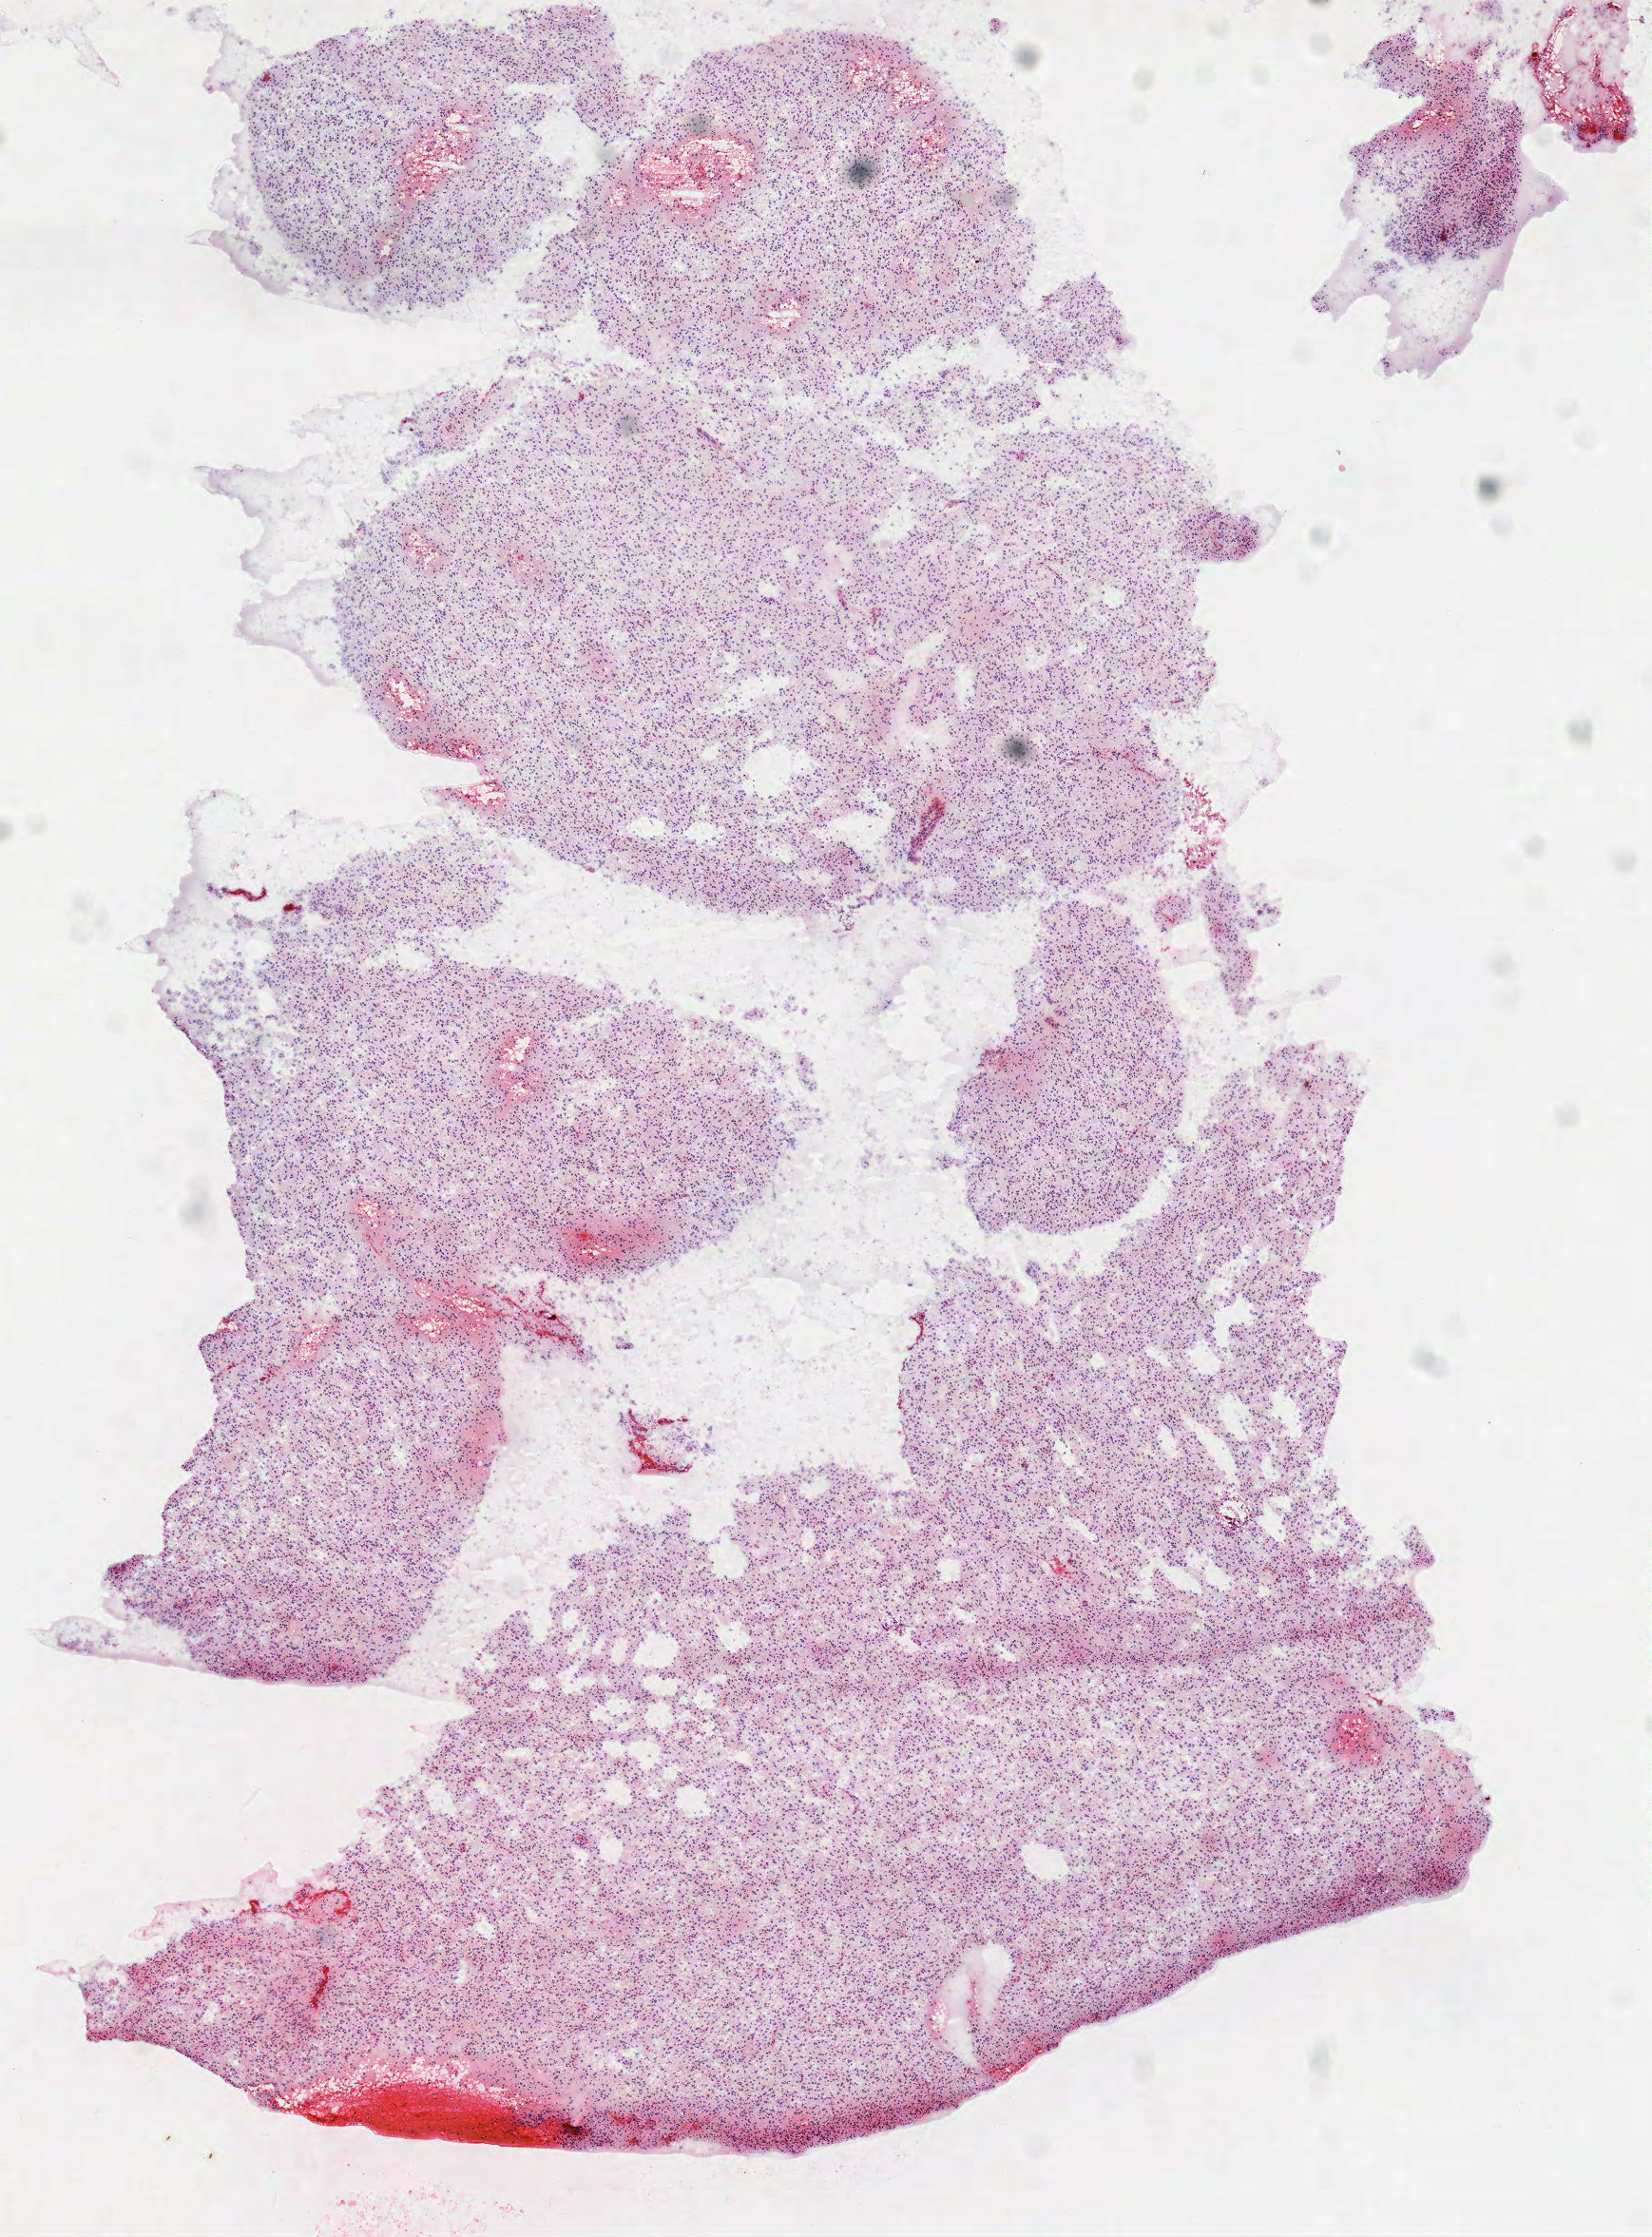
Digitized Hematoxylin and eosin (H&E) stained tissue section (whole slide), low-resolution overview of the scanned area, about 7.0 x 9.5 mm. Frozen section from the top of the tissue portion. Sample: primary tumour, brain. Male patient; age at initial diagnosis 35 years. Histologic grade: G2 (moderately differentiated). Slide review estimates, as recorded: tumour cells 100%, tumour nuclei 80%, normal cells 0%, stromal cells 0%, necrosis 0%.
Histologic diagnosis: Oligodendroglioma, NOS (cerebrum).